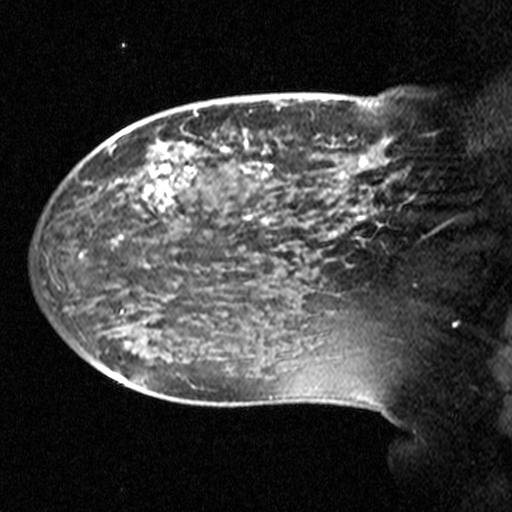
Breast MRI (dynamic contrast-enhanced), one sagittal slice. Position 13 of 44 along the scan axis. Dynamic contrast-enhanced study with each time point stored as its own series, time point 2 of 3 at this slice position (early post-contrast, ordered by acquisition time). 1.5 T. TE 4.5 ms, TR 11 ms. 512 × 512 image matrix, field of view 240 × 240 mm. Female patient, age 38 years. From the clinical record (not read from this slice): setting: breast cancer imaged before/during neoadjuvant chemotherapy; receptor status: HR-positive, HER2-negative.
Annotated regions visible in this slice (semi-automatically segmented with operator editing):
- analysis volume of interest (the breast-tissue region the enhancement analysis was run in; not a lesion): box from (x=124, y=106) to (x=405, y=245) px
- tumour enhancement mask (voxels above the 90 % enhancement threshold inside the analysis volume of interest): (x=147, y=148)–(x=272, y=194)